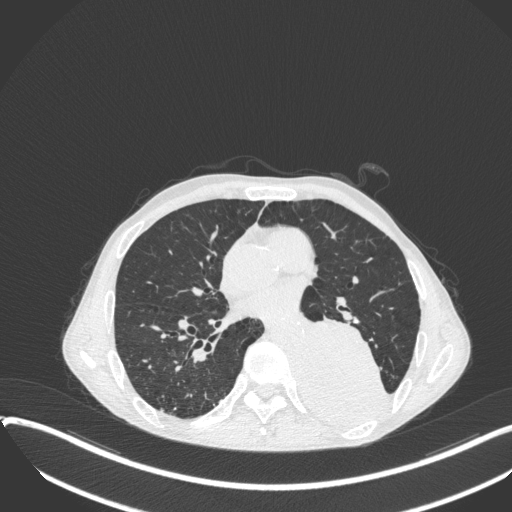
Chest CT, one axial slice. Slice 174 of 400 in the series (ordered by position). Reconstruction kernel B31f. Lung window (W 1500 / L -600 HU). 1 mm slice thickness. 512 × 512 image matrix, field of view 400 × 400 mm. Patient: male, 57 years. From the clinical record (not read from this slice): clinical TNM (as recorded): T4 N0 M0.
Structures marked on this image (bounding box drawn by a radiologist):
- lung tumour (recorded histology: squamous cell carcinoma): bounding box <301,314,391,429> (left, top, right, bottom; pixels)